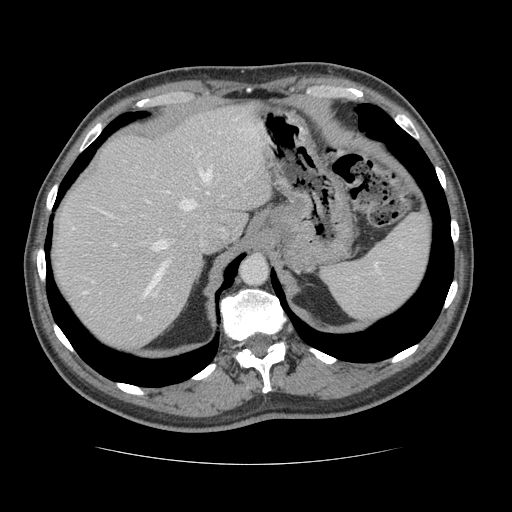
Contrast-enhanced abdominal CT, one axial slice; slice 100 of 134 in the series (ordered by position); reconstruction kernel STANDARD; intravenous contrast given; soft-tissue window (W 400 / L 40 HU); 512 × 512 image matrix, field of view 377 × 377 mm. Male patient, age 68 years. Case-level facts recorded for this patient, not image findings: diagnosis: colorectal cancer liver metastases, imaged before liver resection; multiple liver metastases: yes; largest metastasis: 2.2 cm; disease in both lobes: no.
Annotated regions visible in this slice (expert manual segmentation):
- hepatic veins: bounding box [x1, y1, x2, y2] px = [83, 170, 211, 319]
- liver: [53, 104, 271, 351]
- planned liver remnant (the part of the liver to remain after resection): [52, 105, 271, 325]
- portal vein (with intrahepatic branches): [113, 243, 156, 296]